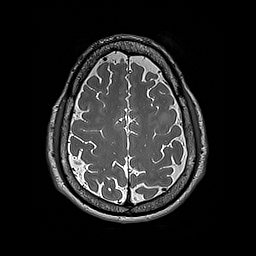
Brain MRI from a brain-tumour surgery series, one axial slice. Position 65 of 192 along the scan axis. 256 × 256 image matrix, field of view 250 × 250 mm. From the clinical record (not read from this slice): histopathology: Astrocytoma; WHO grade: 2; IDH mutation: yes.
Structures marked on this image (outlined manually by an expert reader):
- tumour: bounding box [x1, y1, x2, y2] px = [159, 111, 171, 123]